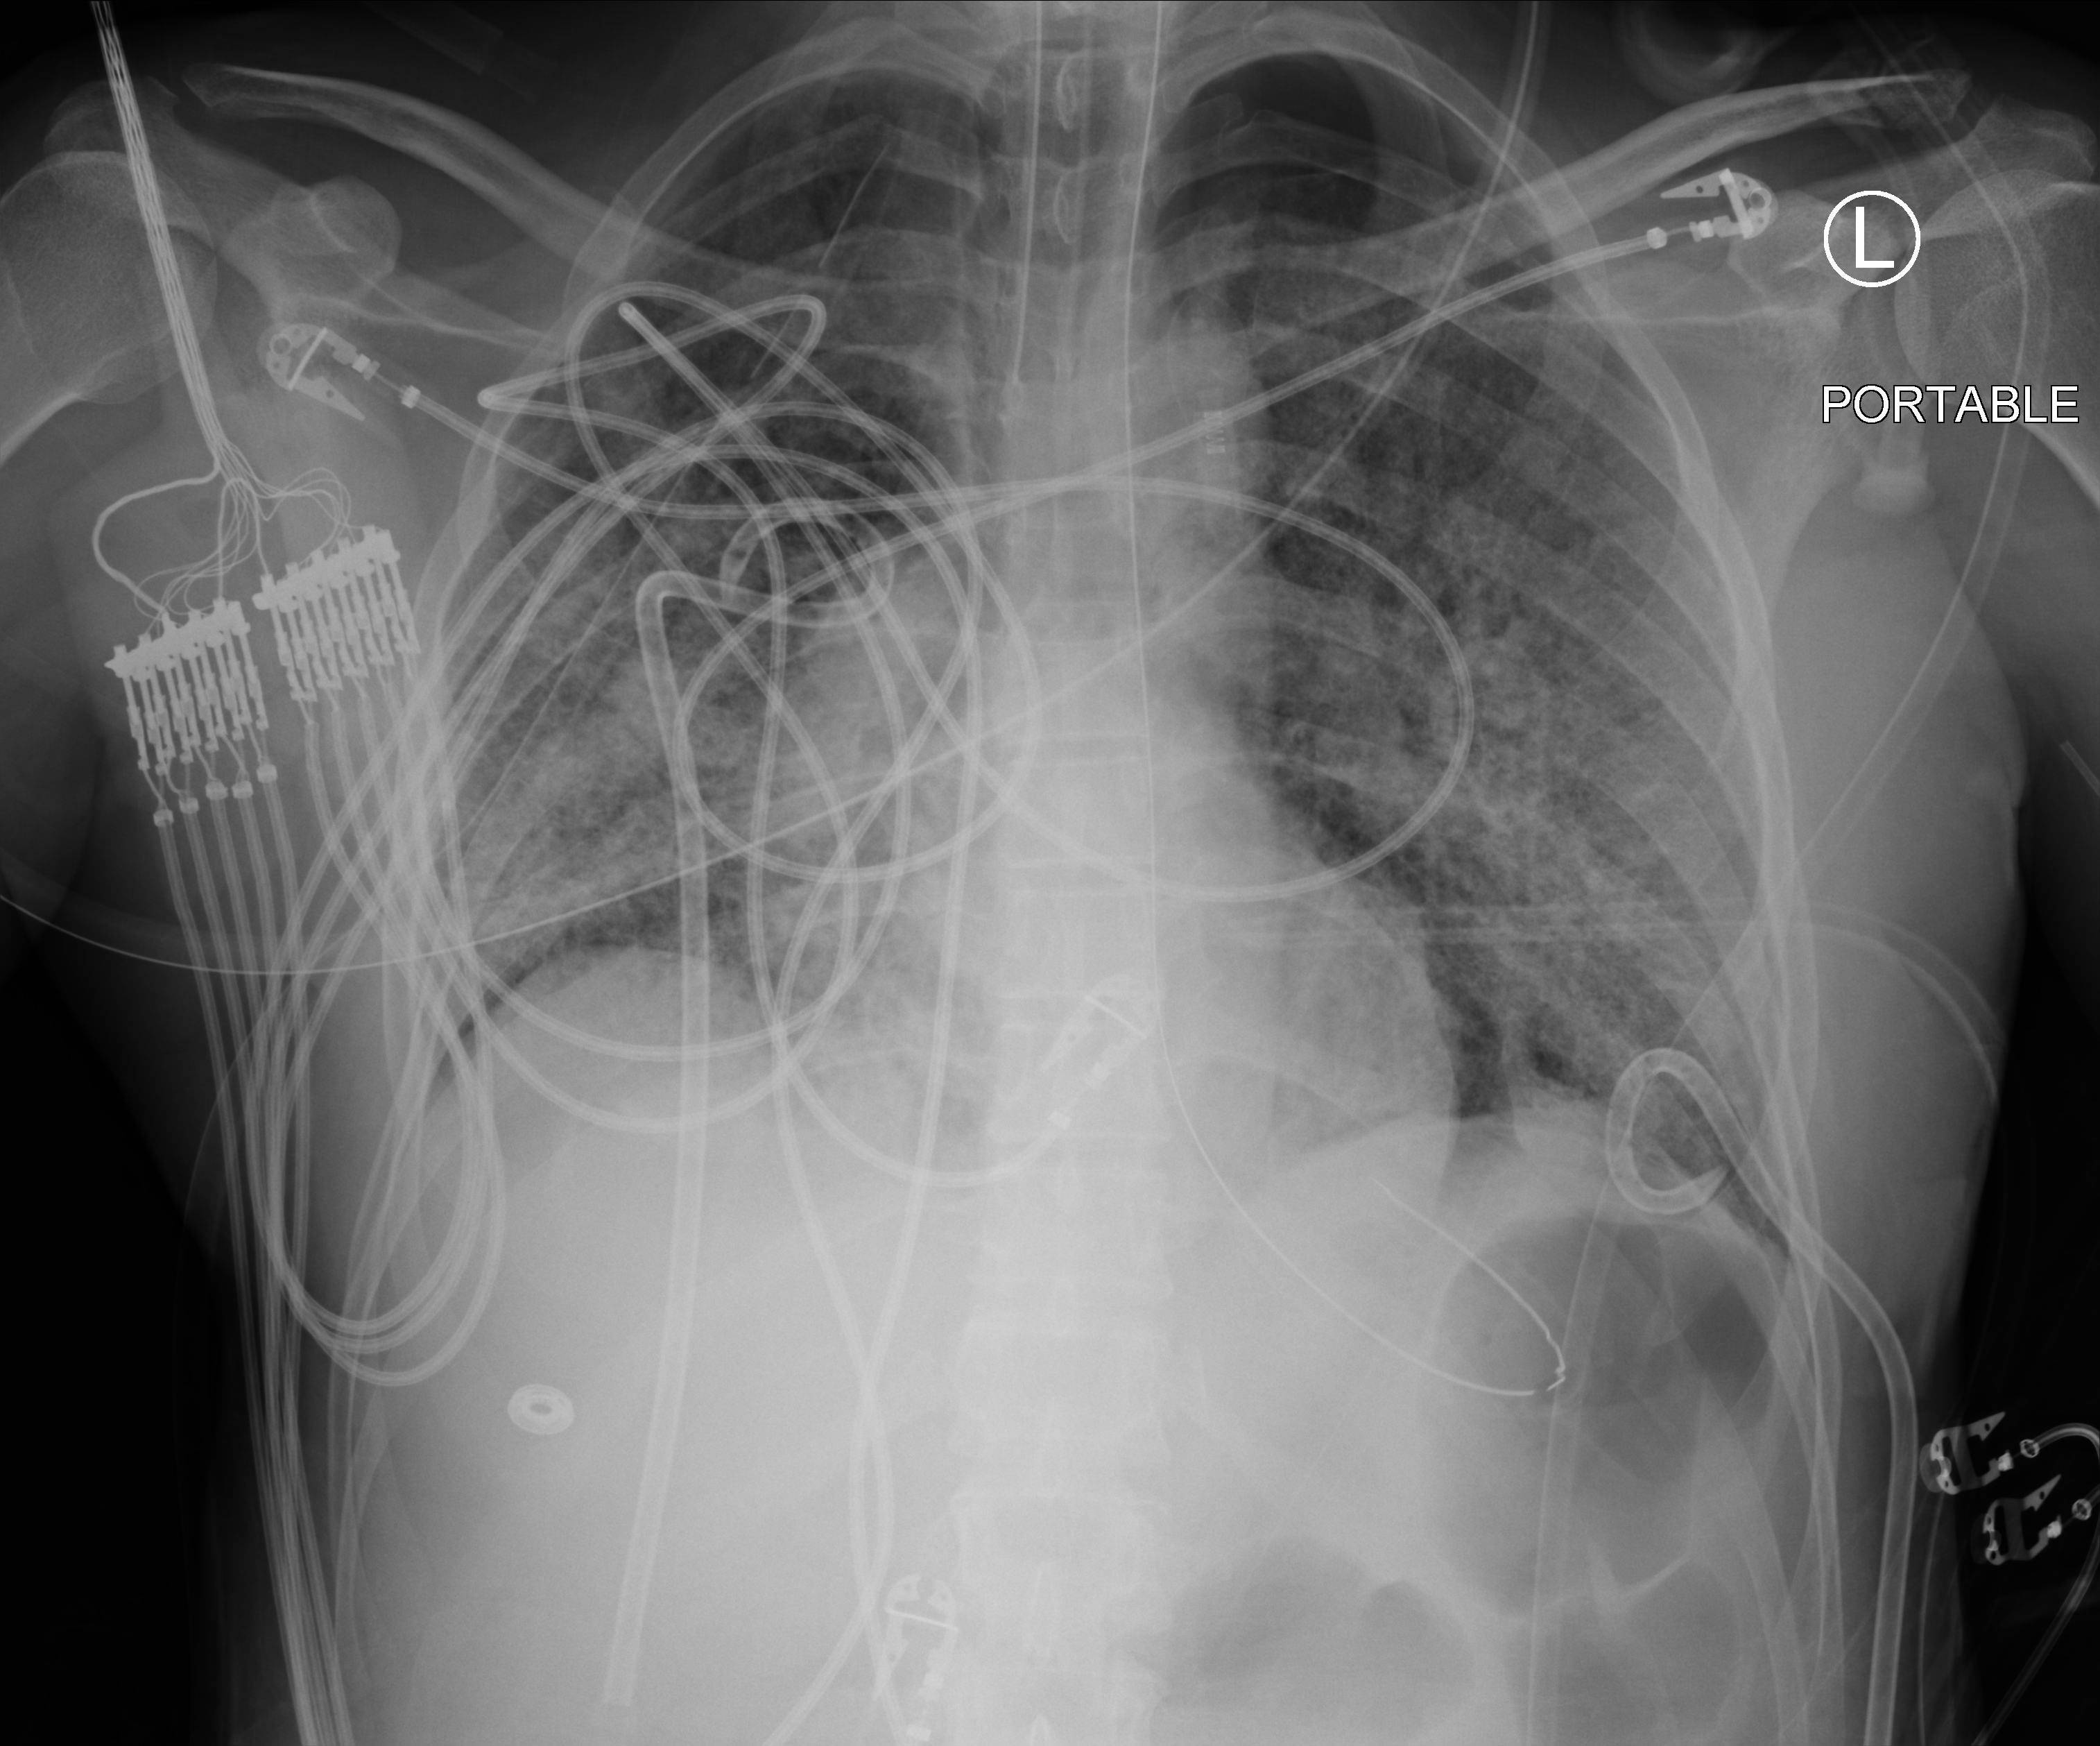
Chest X-ray (portable), anteroposterior (AP) projection. Adult patient hospitalised with COVID-19, age 18–59 years.
From the hospital-stay record, not from the radiograph (when in the stay this image was taken is not recorded): COPD (admission record): no; mechanically ventilated during this hospital stay: yes.